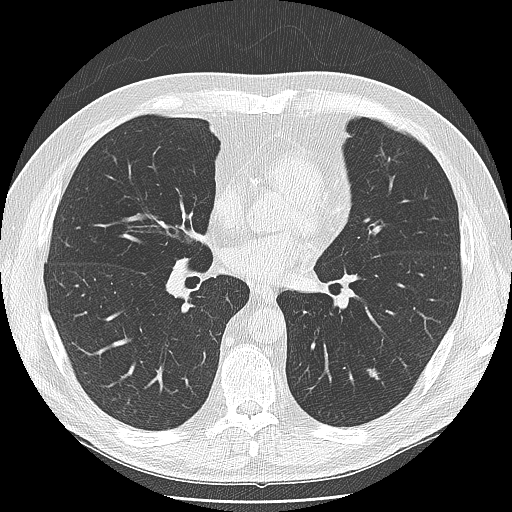
Low-dose screening chest CT, one axial slice. Position 81 of 166 along the scan axis. 120 kVp. Lung window (W 1500 / L -600 HU). 2.5 mm slice thickness. 512 × 512 image matrix, field of view 360 × 360 mm.
Structures marked on this image (outlined manually by an expert reader):
- lesion 1 (tumor, lower lobe of left lung): bounding box <367,368,380,380> (left, top, right, bottom; pixels)